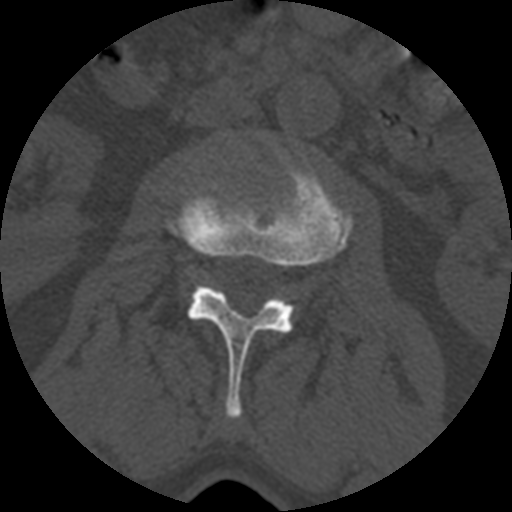
CT including the spine, one axial slice. Position 328 of 399 along the scan axis. 120 kVp. Bone window (W 1800 / L 400 HU). 1.25 mm slice thickness. 512 × 512 image matrix, field of view 160 × 160 mm. Patient age 71 years. From the clinical record (not read from this slice): primary cancer: prostate.
Structures marked on this image (semi-automatically segmented with operator editing):
- L2 vertebra: bounding box (x1, y1, x2, y2) in pixels: (169, 167, 352, 421)